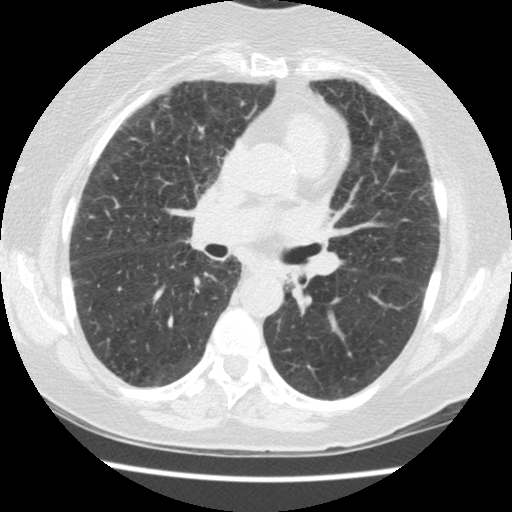
Chest CT (low-dose screening protocol), one axial image. Second screening round (one year after baseline). Lung window (W 1500 / L -600 HU). 2.5 mm slice thickness. Slice 61 of 134 in the series. Female participant, aged 60 years at enrolment.
Expert-annotated lung lesion, bounding box (x1, y1, x2, y2) in pixels: (268, 258, 316, 303). Reader record for this screening exam (exam-level; its link to the box is not recorded): non-calcified nodule or mass ≥4 mm, left lower lobe, 5 × 4 mm, smooth margins, soft tissue attenuation, pre-existing on the prior screen: yes; interval growth: no. Official screen result: positive, no significant change: stable abnormalities potentially related to lung cancer, unchanged since the prior screening exam. Participant outcome: lung cancer diagnosed 423 days after this screen (after the third annual screen) — small cell carcinoma, NOS, left lower lobe, undifferentiated (G4), stage IV (AJCC 6th edition), 69 mm at pathology.